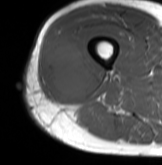
MRI of an extremity soft-tissue mass, one axial slice. Slice 30 of 61 in the series (ordered by position). MR volume resampled by the dataset authors to the PET/CT grid (not the native acquisition matrix). 3.27 mm slice thickness. 162 × 165 image matrix, field of view 158 × 161 mm. Male patient. From the clinical record (not read from this slice): histological type: poorly differentiated synovial sarcoma; grade: high; site of the primary tumour: right buttock.
Structures marked on this image (expert contour drawn on MRI and transferred to this co-registered scan by the dataset authors):
- gross tumour volume including surrounding oedema: bounding box [x1, y1, x2, y2] px = [43, 31, 94, 101]
- gross tumour volume (mass): [45, 40, 94, 101]